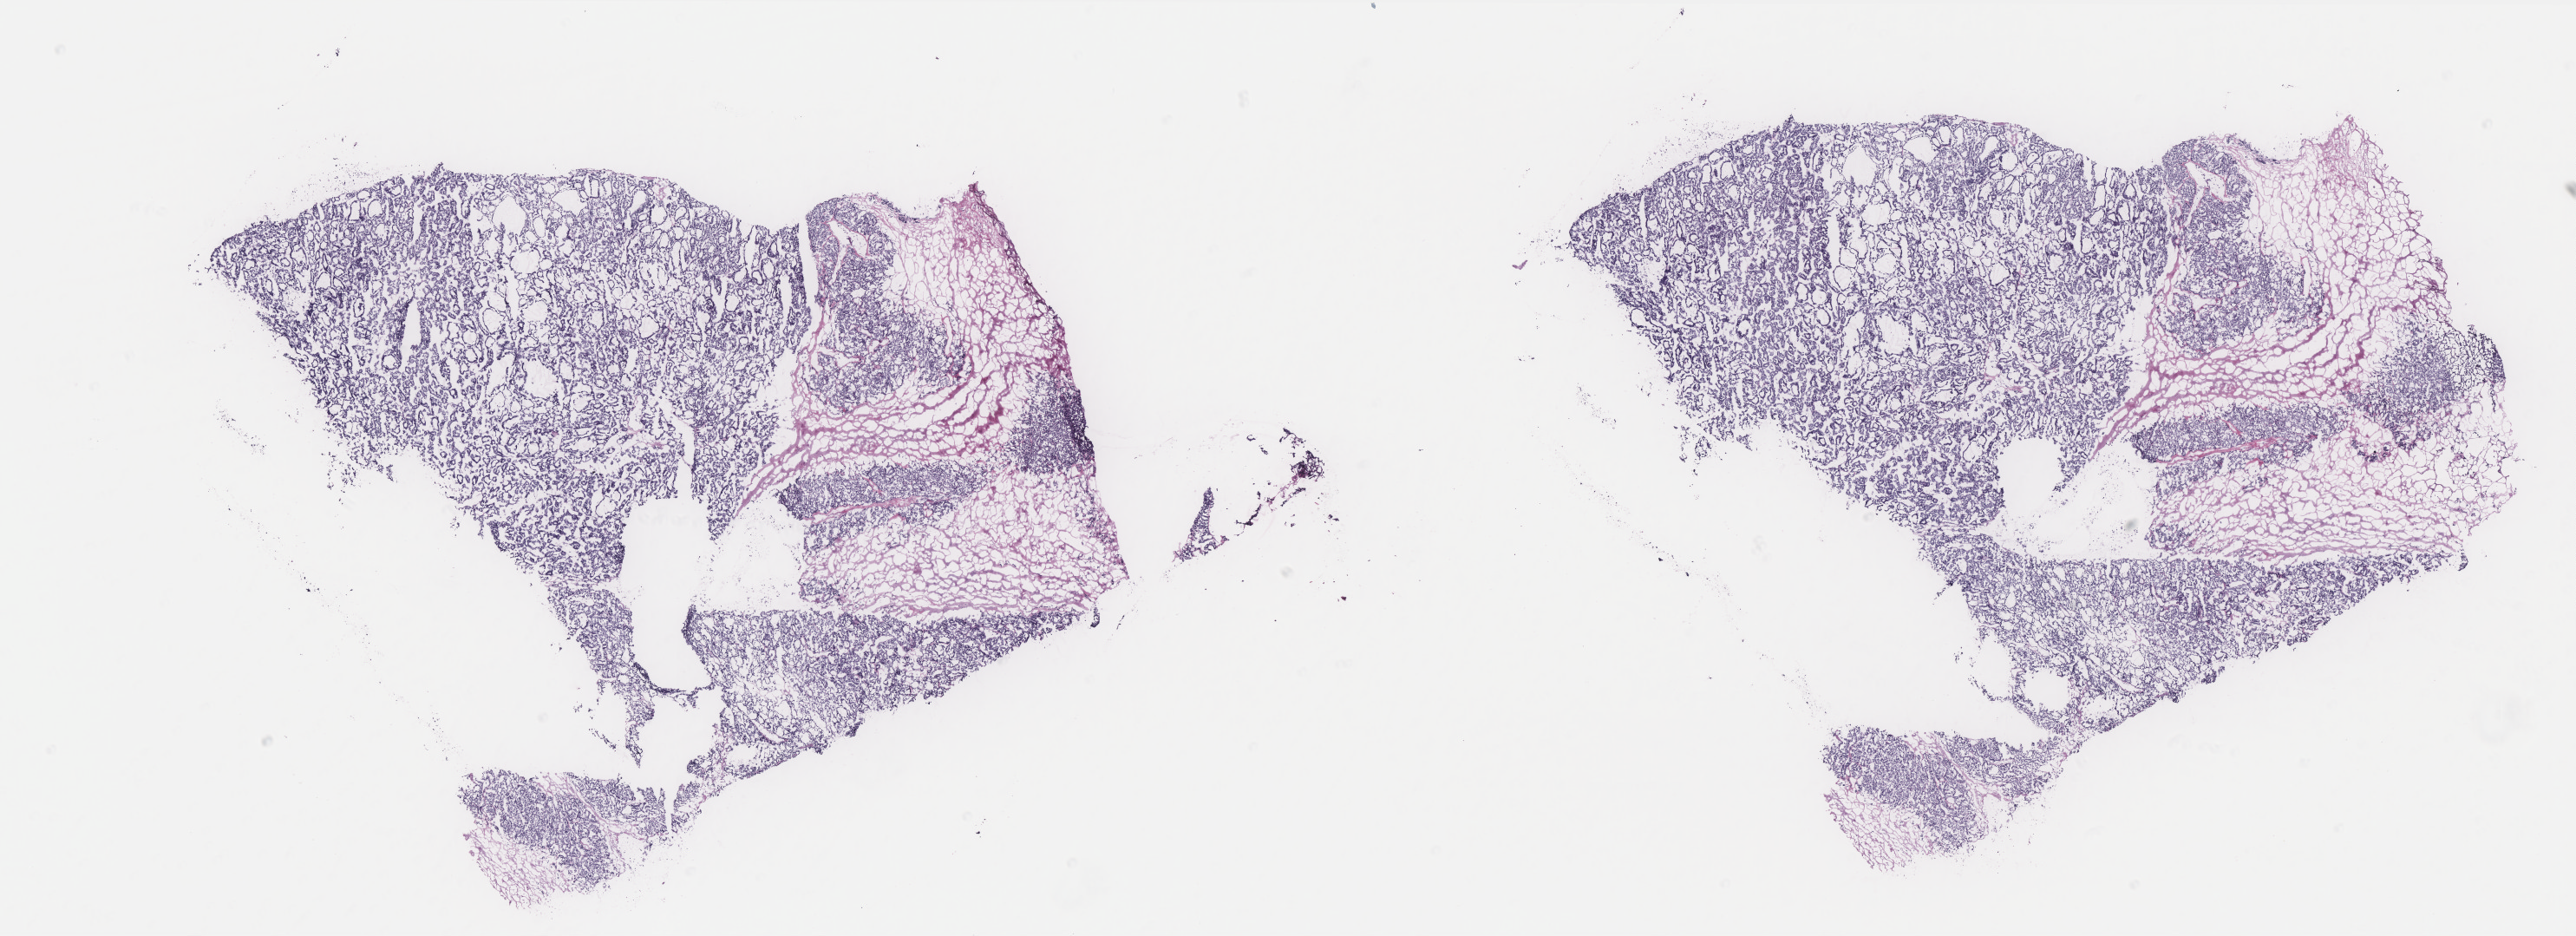
Hematoxylin and eosin (H&E) stained whole-slide image, low-resolution overview of the scanned area, about 23.8 x 8.7 mm (from a 40x scan). Frozen section from the top of the tissue portion. Sample: primary tumour, thyroid. Male, age 57 years at initial diagnosis. Pathologist review of this section (percent, as recorded): tumour cells 85%, tumour nuclei 97%, normal cells 0%, stromal cells 15%, necrosis 0%. Infiltration values recorded for this section: lymphocyte infiltration 0%, monocyte infiltration 0%, neutrophil infiltration 0%.
Diagnosis: Follicular adenocarcinoma, NOS (thyroid gland). AJCC pathologic stage: IVC (7th edition).